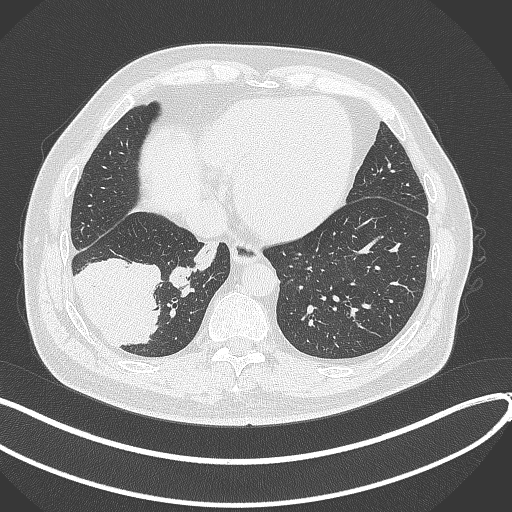
Chest CT, one axial slice; slice 96 of 360 in the series (ordered by position); 120 kVp; lung window (W 1500 / L -600 HU); 1 mm slice thickness; 512 × 512 image matrix. Male patient, age 59 years.
Annotated regions visible in this slice (rectangle marked by the reading radiologist):
- lung tumour (recorded histology: adenocarcinoma): bounding box (x1, y1, x2, y2) in pixels: (73, 253, 165, 347)